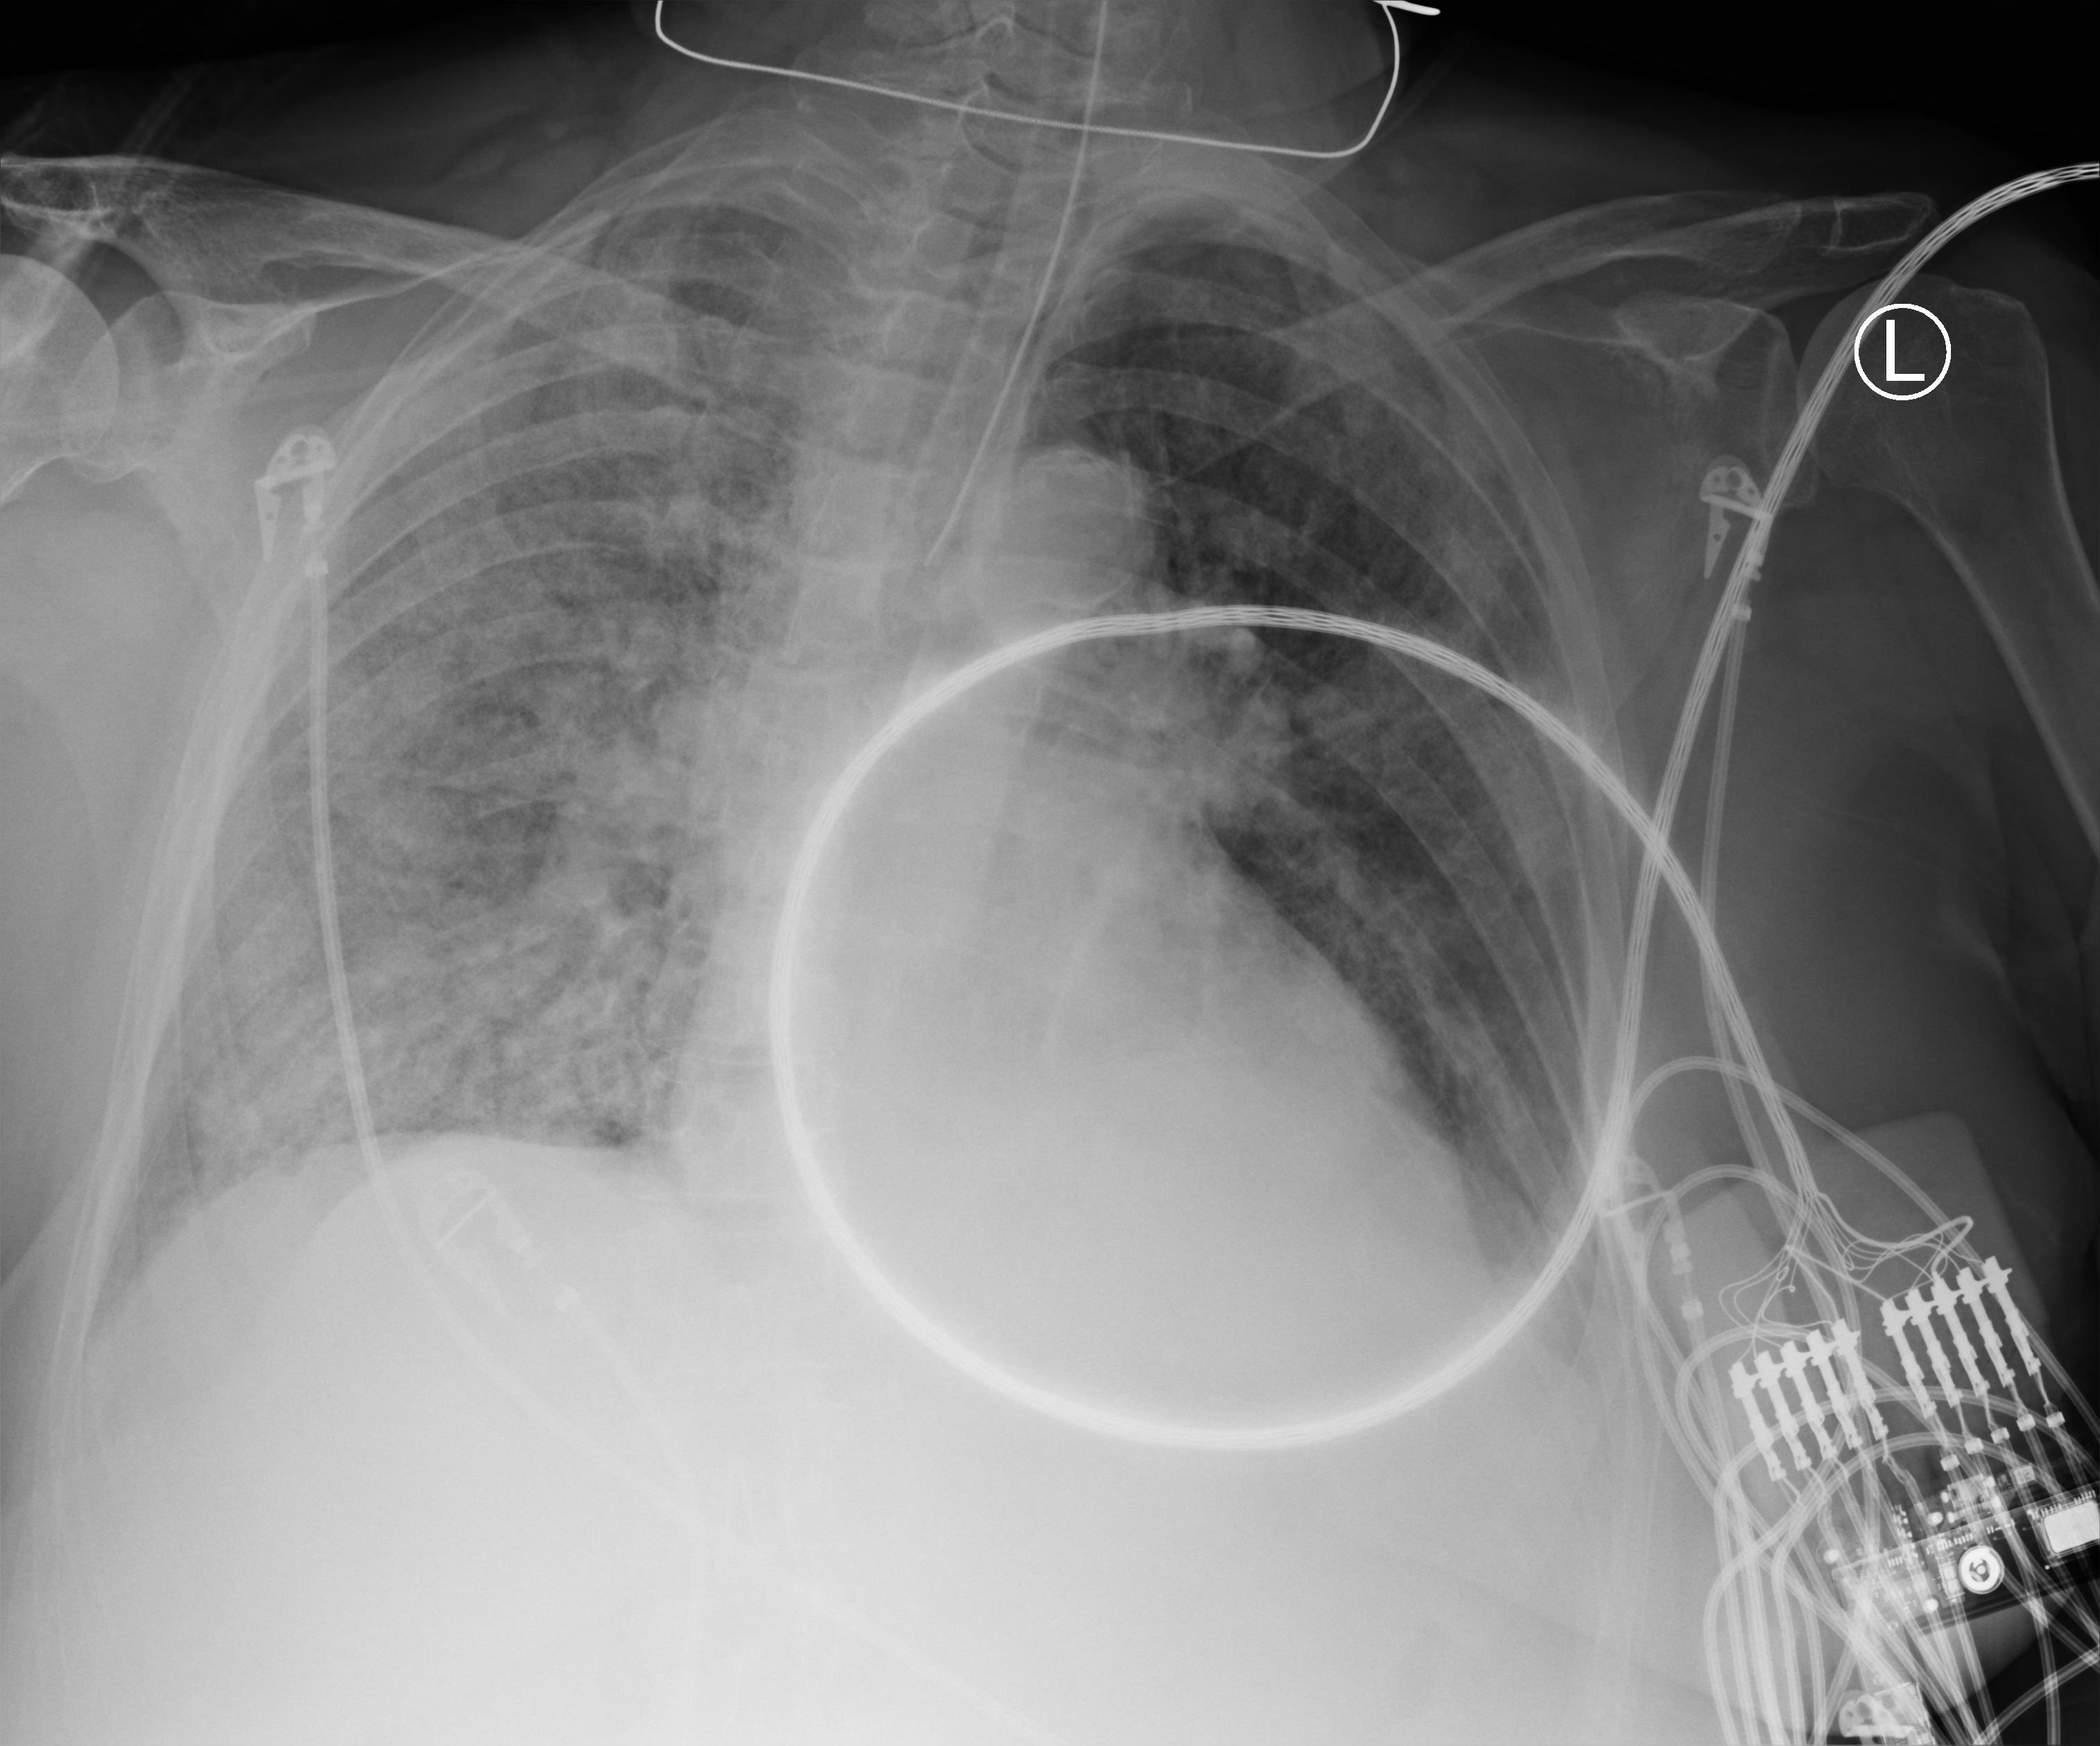
Portable chest radiograph, anteroposterior (AP) projection. Patient hospitalised with COVID-19; female, aged 75–90 years.
From the hospital-stay record, not from the radiograph (when in the stay this image was taken is not recorded):
- smoking status (admission record): former
- mechanically ventilated during this hospital stay: yes